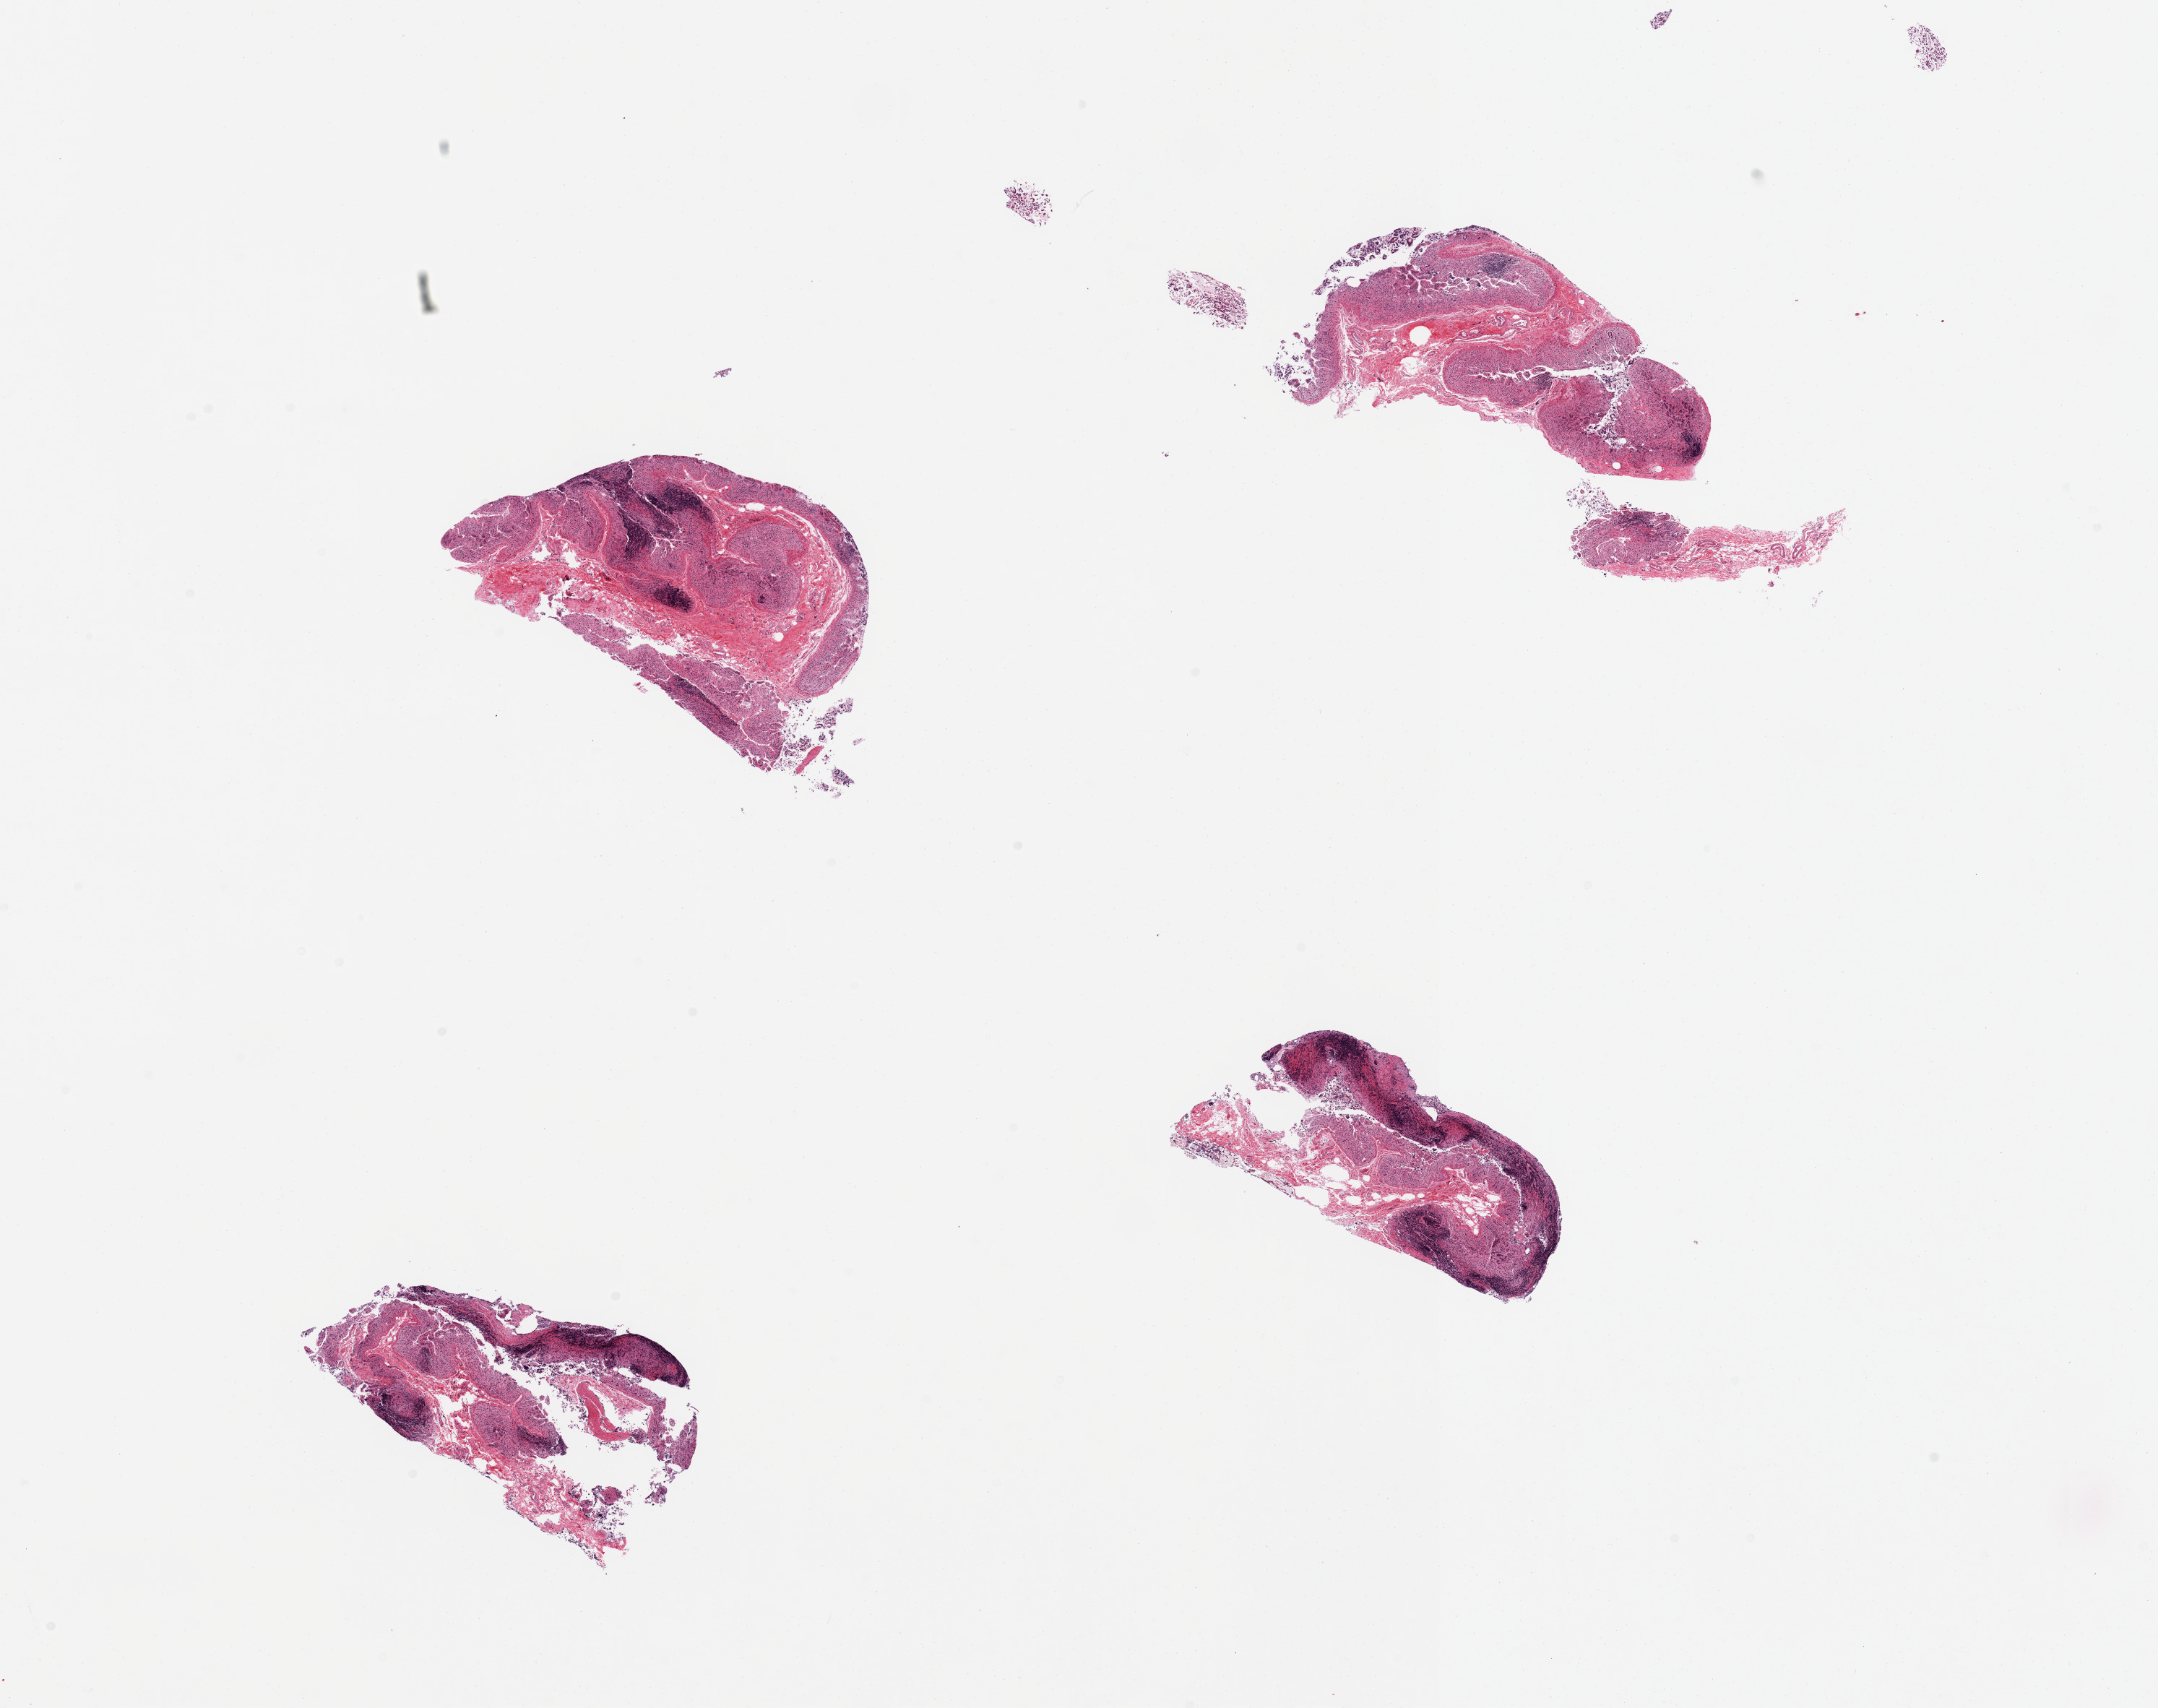
Whole-slide image, H&E stain, whole scanned area (about 23.6 x 18.7 mm) shown as a low-resolution overview, PAXgene-fixed, paraffin-embedded tissue, section of ileum (target tissue), donor tissue sample.
Review note (as recorded): 4 pieces, mucosa autolyzed, ~20% residual lymphoid elements present.